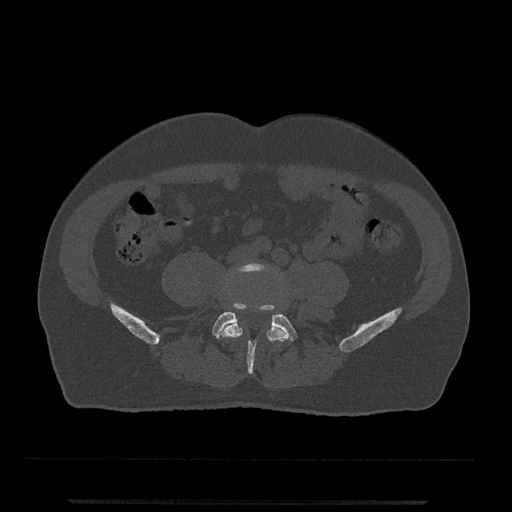
CT including the spine, one axial slice; position 99 of 797 along the scan axis; 120 kVp; bone window (W 1800 / L 400 HU); 0.5 mm slice thickness; 512 × 512 image matrix, field of view 419 × 419 mm. Male patient, age 63 years. Case-level facts recorded for this patient, not image findings: primary cancer: prostate.
Structures marked on this image (semi-automatically segmented with operator editing):
- L4 vertebra: bounding box (x1, y1, x2, y2) in pixels: (221, 262, 289, 372)
- L5 vertebra: (212, 303, 298, 374)